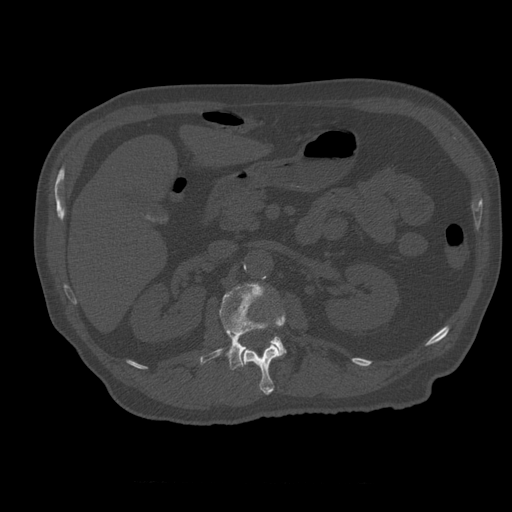
CT including the spine, one axial slice; slice 226 of 399 in the series (ordered by position); reconstruction kernel STANDARD; 120 kVp; bone window (W 1800 / L 400 HU); 1.25 mm slice thickness; 512 × 512 image matrix, field of view 407 × 407 mm. Patient age 73 years. Case-level facts recorded for this patient, not image findings: primary cancer: prostate.
Structures marked on this image (semi-automatic segmentation, software-assisted and operator-edited):
- L1 vertebra: bounding box (x1, y1, x2, y2) in pixels: (241, 316, 285, 395)
- L2 vertebra: (200, 283, 287, 370)